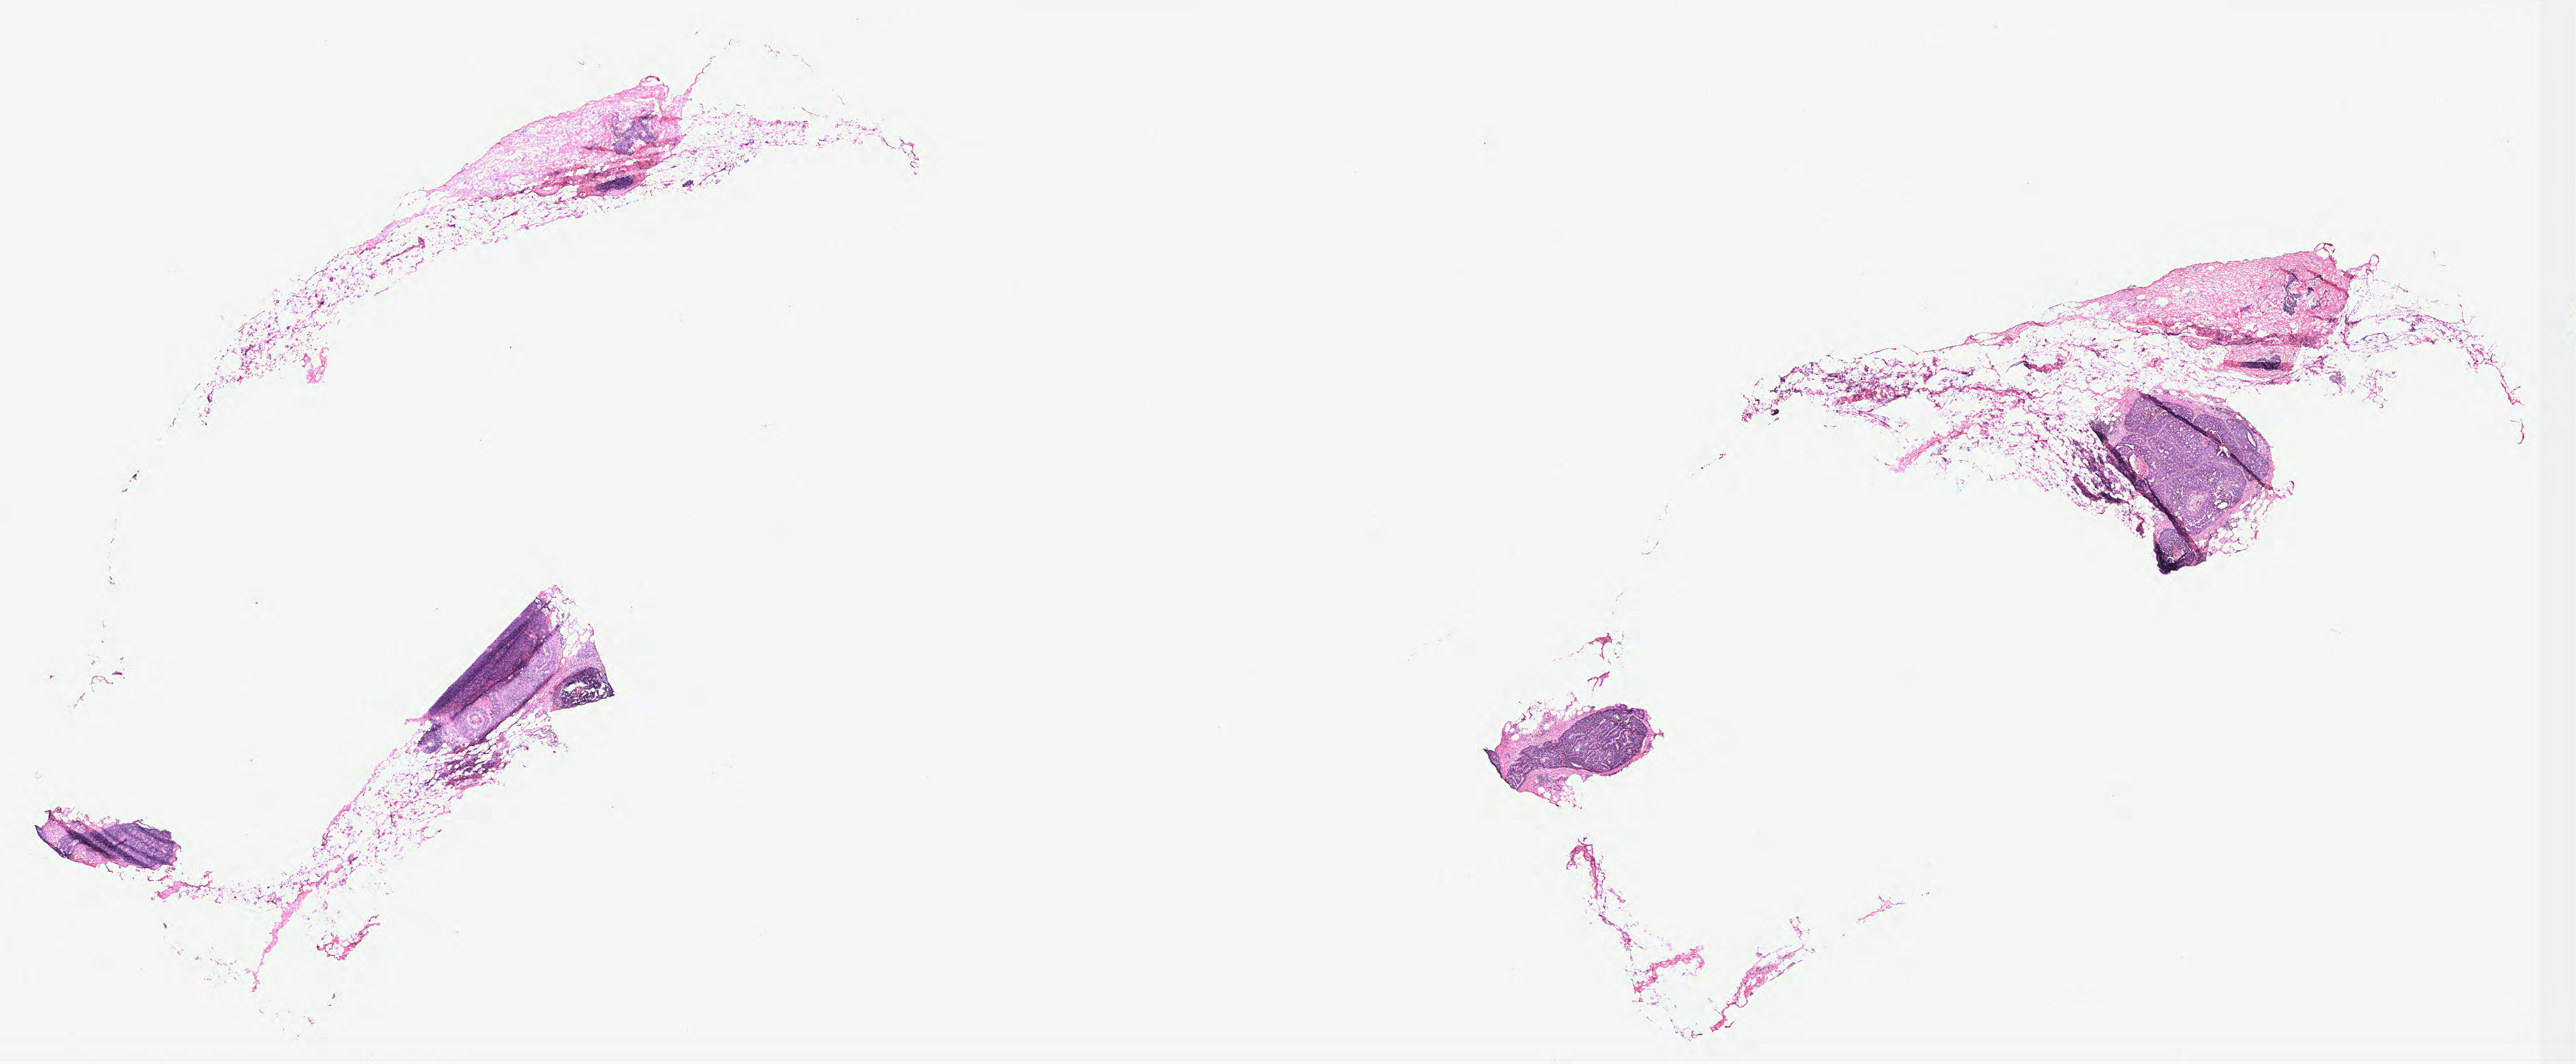
Hematoxylin and eosin (H&E) stained whole-slide image, low-resolution overview of the scanned area, about 32.2 x 13.3 mm, breast, tissue type not recorded. Patient: female, age 54 years.
* patient diagnosis: Infiltrating duct carcinoma, NOS